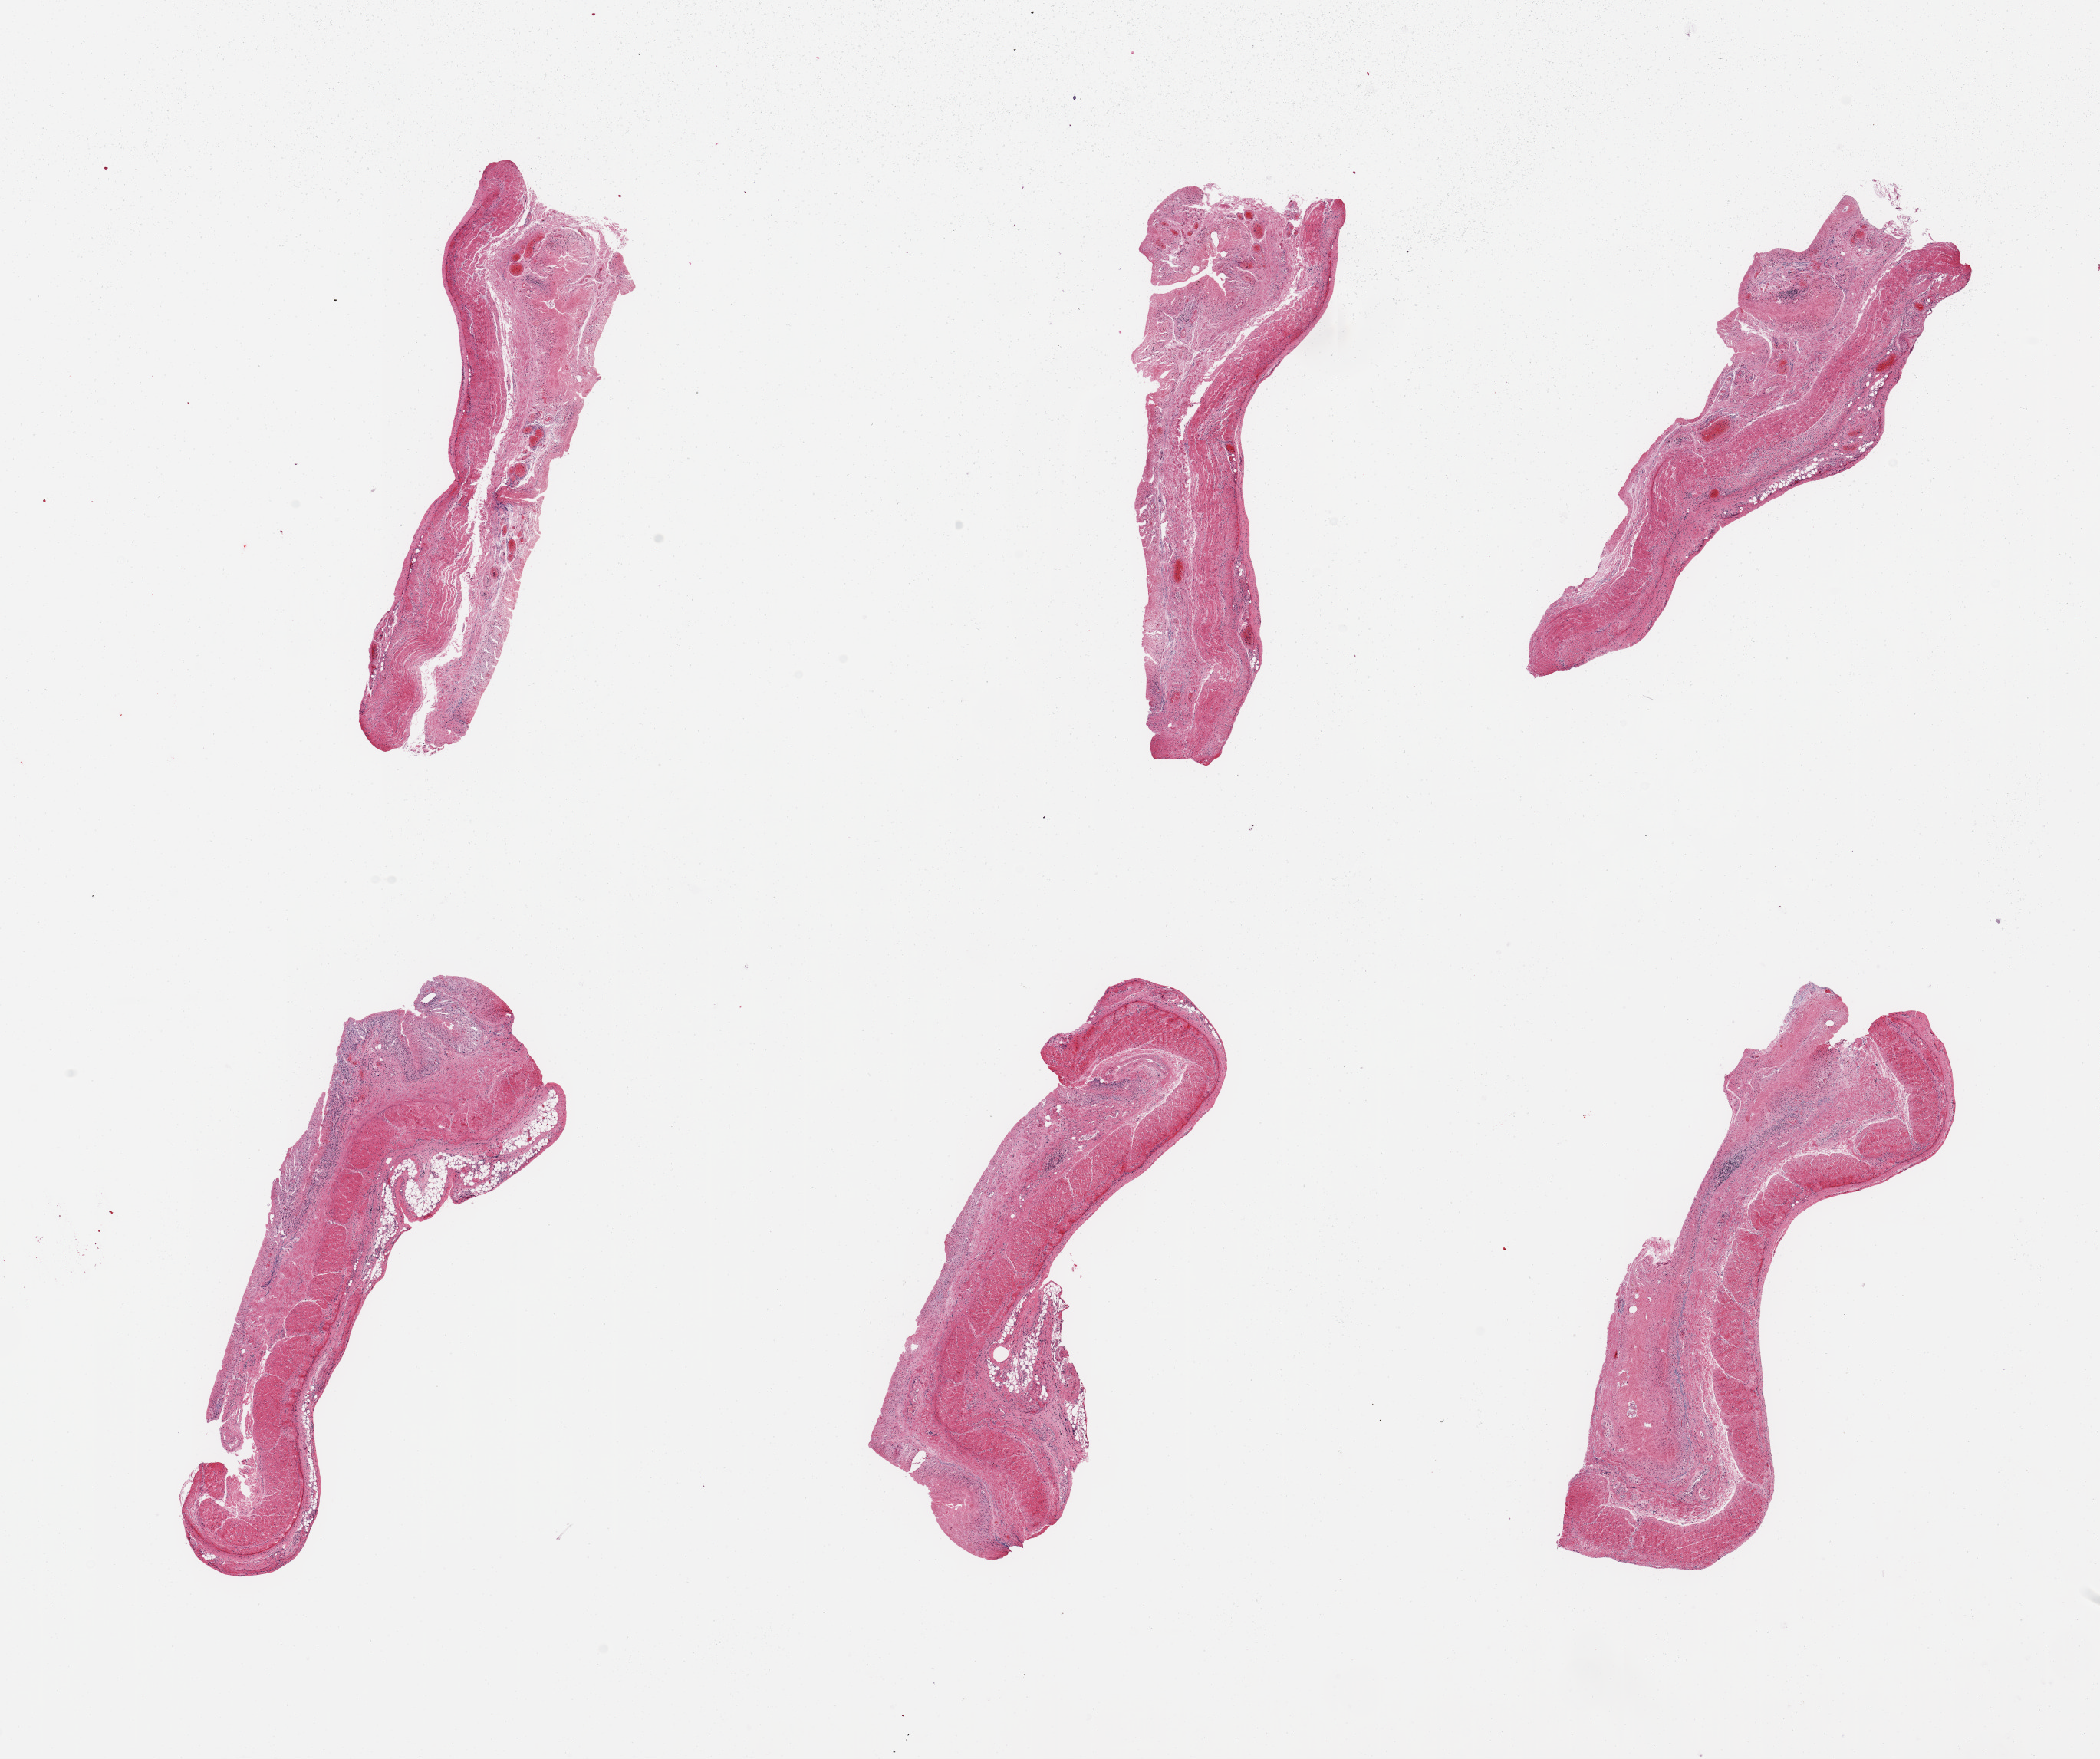
H&E whole-slide image, brightfield, whole scanned area (about 21.7 x 18.1 mm) shown as a low-resolution overview, PAXgene-fixed paraffin-embedded (PFPE) section, sampled site (target tissue): transverse colon, donor tissue sample. Donor sex: female.
Review note (as recorded): 6 pieces, target mucosa up to ~0.25mm, advanced autolysis with epithelial mucosa largely sloughed.